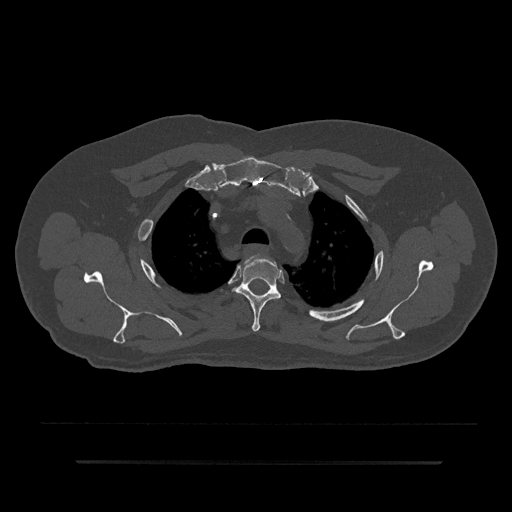
CT including the spine, one axial slice; slice 657 of 797 in the series (ordered by position); reconstruction kernel Br40s/3; bone window (W 1800 / L 400 HU); 0.5 mm slice thickness; 512 × 512 image matrix, field of view 464 × 464 mm. Male patient, age 59 years. From the clinical record (not read from this slice): primary cancer: bile ducts; vertebrae with lytic lesions (as recorded): T10.
Structures marked on this image (semi-automatically segmented with operator editing):
- T3 vertebra: box from (x=232, y=255) to (x=281, y=332) px